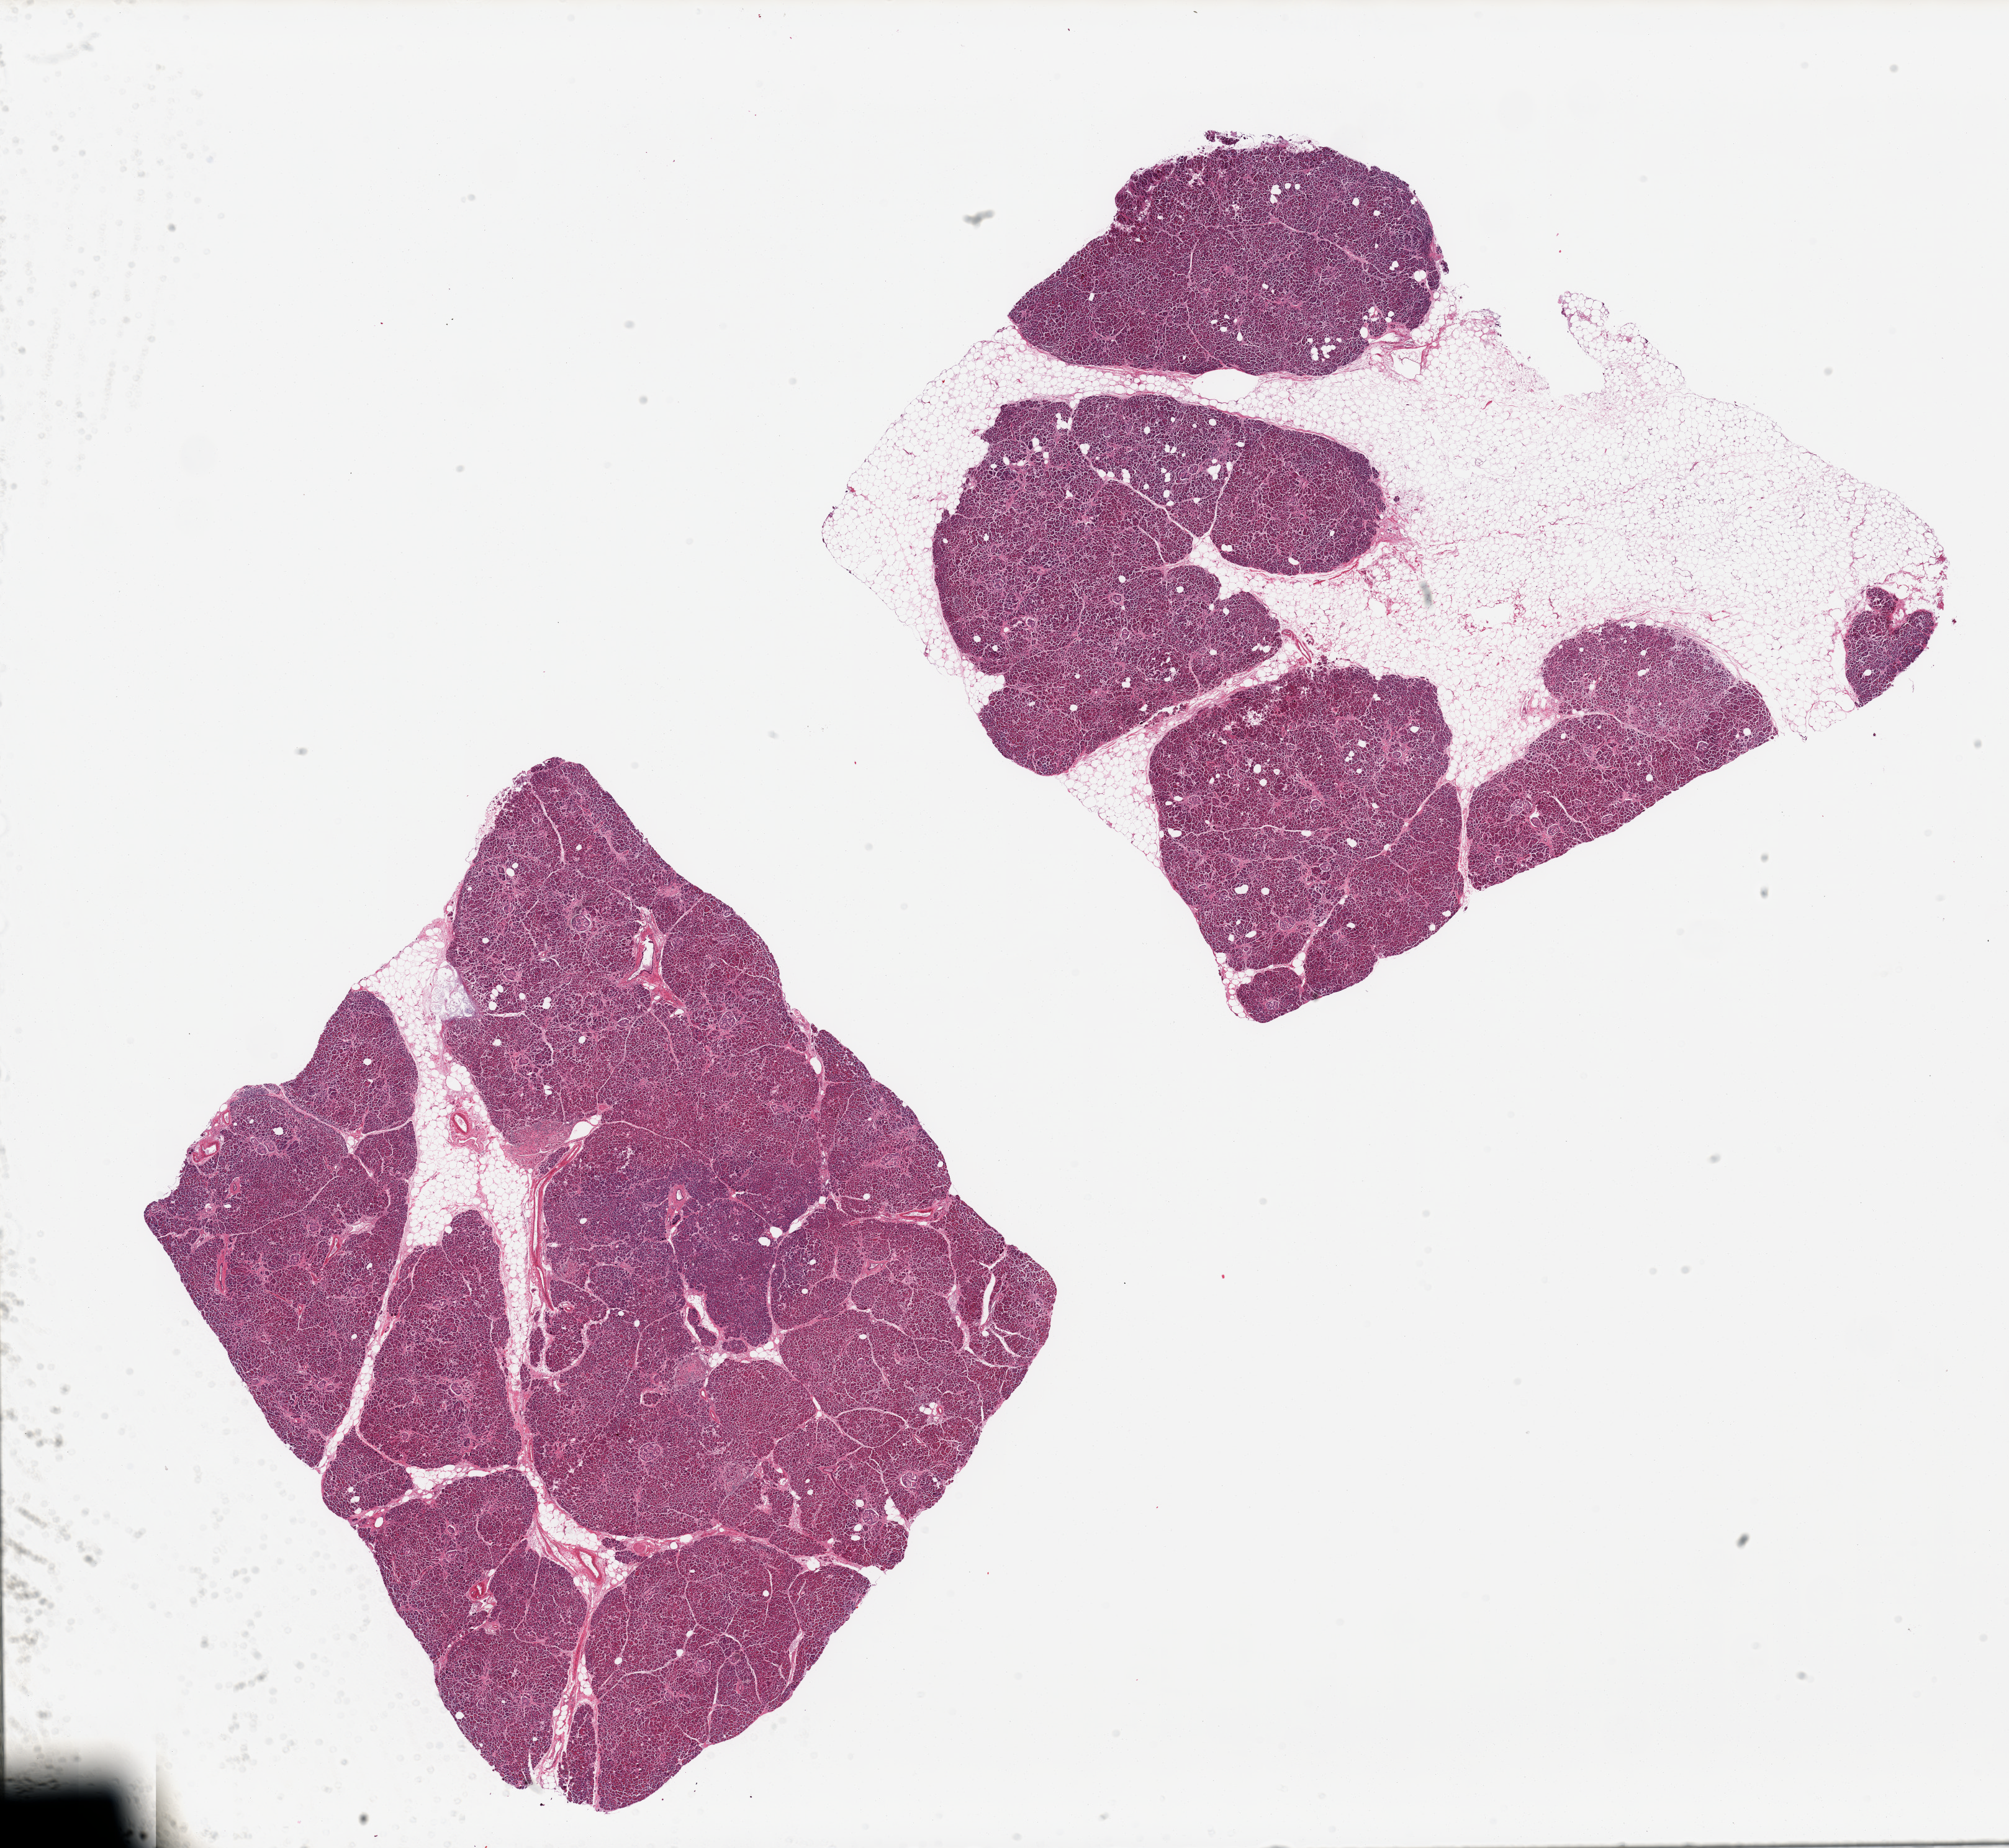
Hematoxylin and eosin (H&E) whole-slide image, shown as a low-resolution overview of the whole scanned area (about 25.6 x 23.5 mm, acquisition: 20x scan). PAXgene-fixed paraffin-embedded (PFPE) section. Sampled site (target tissue): pancreas. Donor tissue sample. Donor: male.
Review note (as recorded): 2 pieces, islets fairly well preserved; ~30% fat.